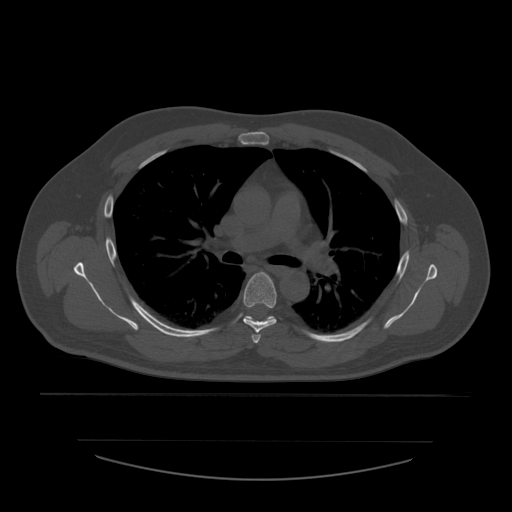
CT including the spine, one axial slice. Position 396 of 532 along the scan axis. 120 kVp. Bone window (W 1800 / L 400 HU). 1.25 mm slice thickness. 512 × 512 image matrix, field of view 441 × 441 mm. Patient age 44 years. From the clinical record (not read from this slice): primary cancer: soft tissue sarcoma.
Structures marked on this image (semi-automatically segmented with operator editing):
- T4 vertebra: box from (x=252, y=335) to (x=261, y=344) px
- T5 vertebra: (x=244, y=272)–(x=277, y=333)
- T6 vertebra: (x=245, y=316)–(x=274, y=322)